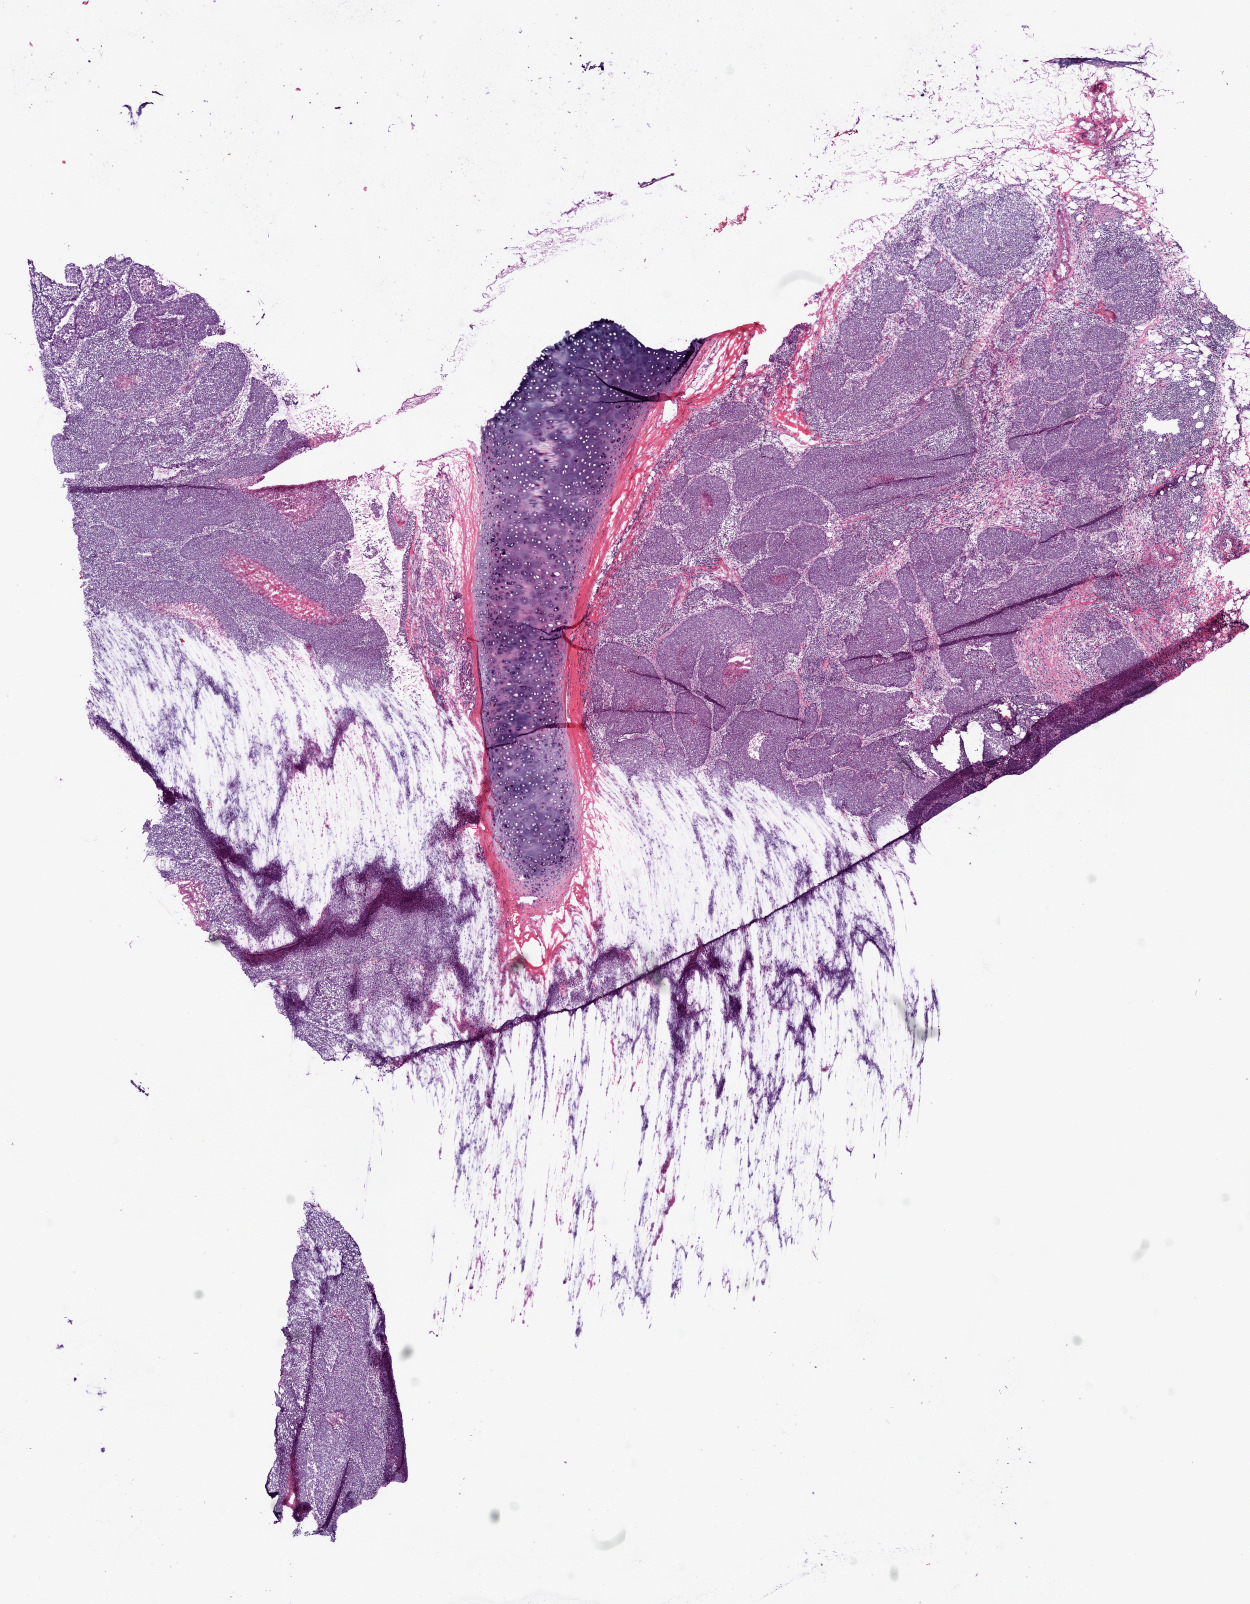
Whole-slide histology image, Hematoxylin and eosin (H&E) stained — shown as a low-resolution overview of the whole scanned area (about 10.0 x 12.9 mm); frozen section from the bottom of the tissue portion; sample: primary tumour, lung. Male patient; age at initial diagnosis 64 years. Composition of this section per pathologist review: tumour cells 75%, tumour nuclei 60%, normal cells 15%, stromal cells 5%, necrosis 5%. Infiltration values recorded for this section: lymphocyte infiltration 30%, monocyte infiltration 0%, neutrophil infiltration 0%.
AJCC pathologic stage: IIIB. Laterality: left. Histologic diagnosis: Squamous cell carcinoma, NOS (upper lobe, lung).